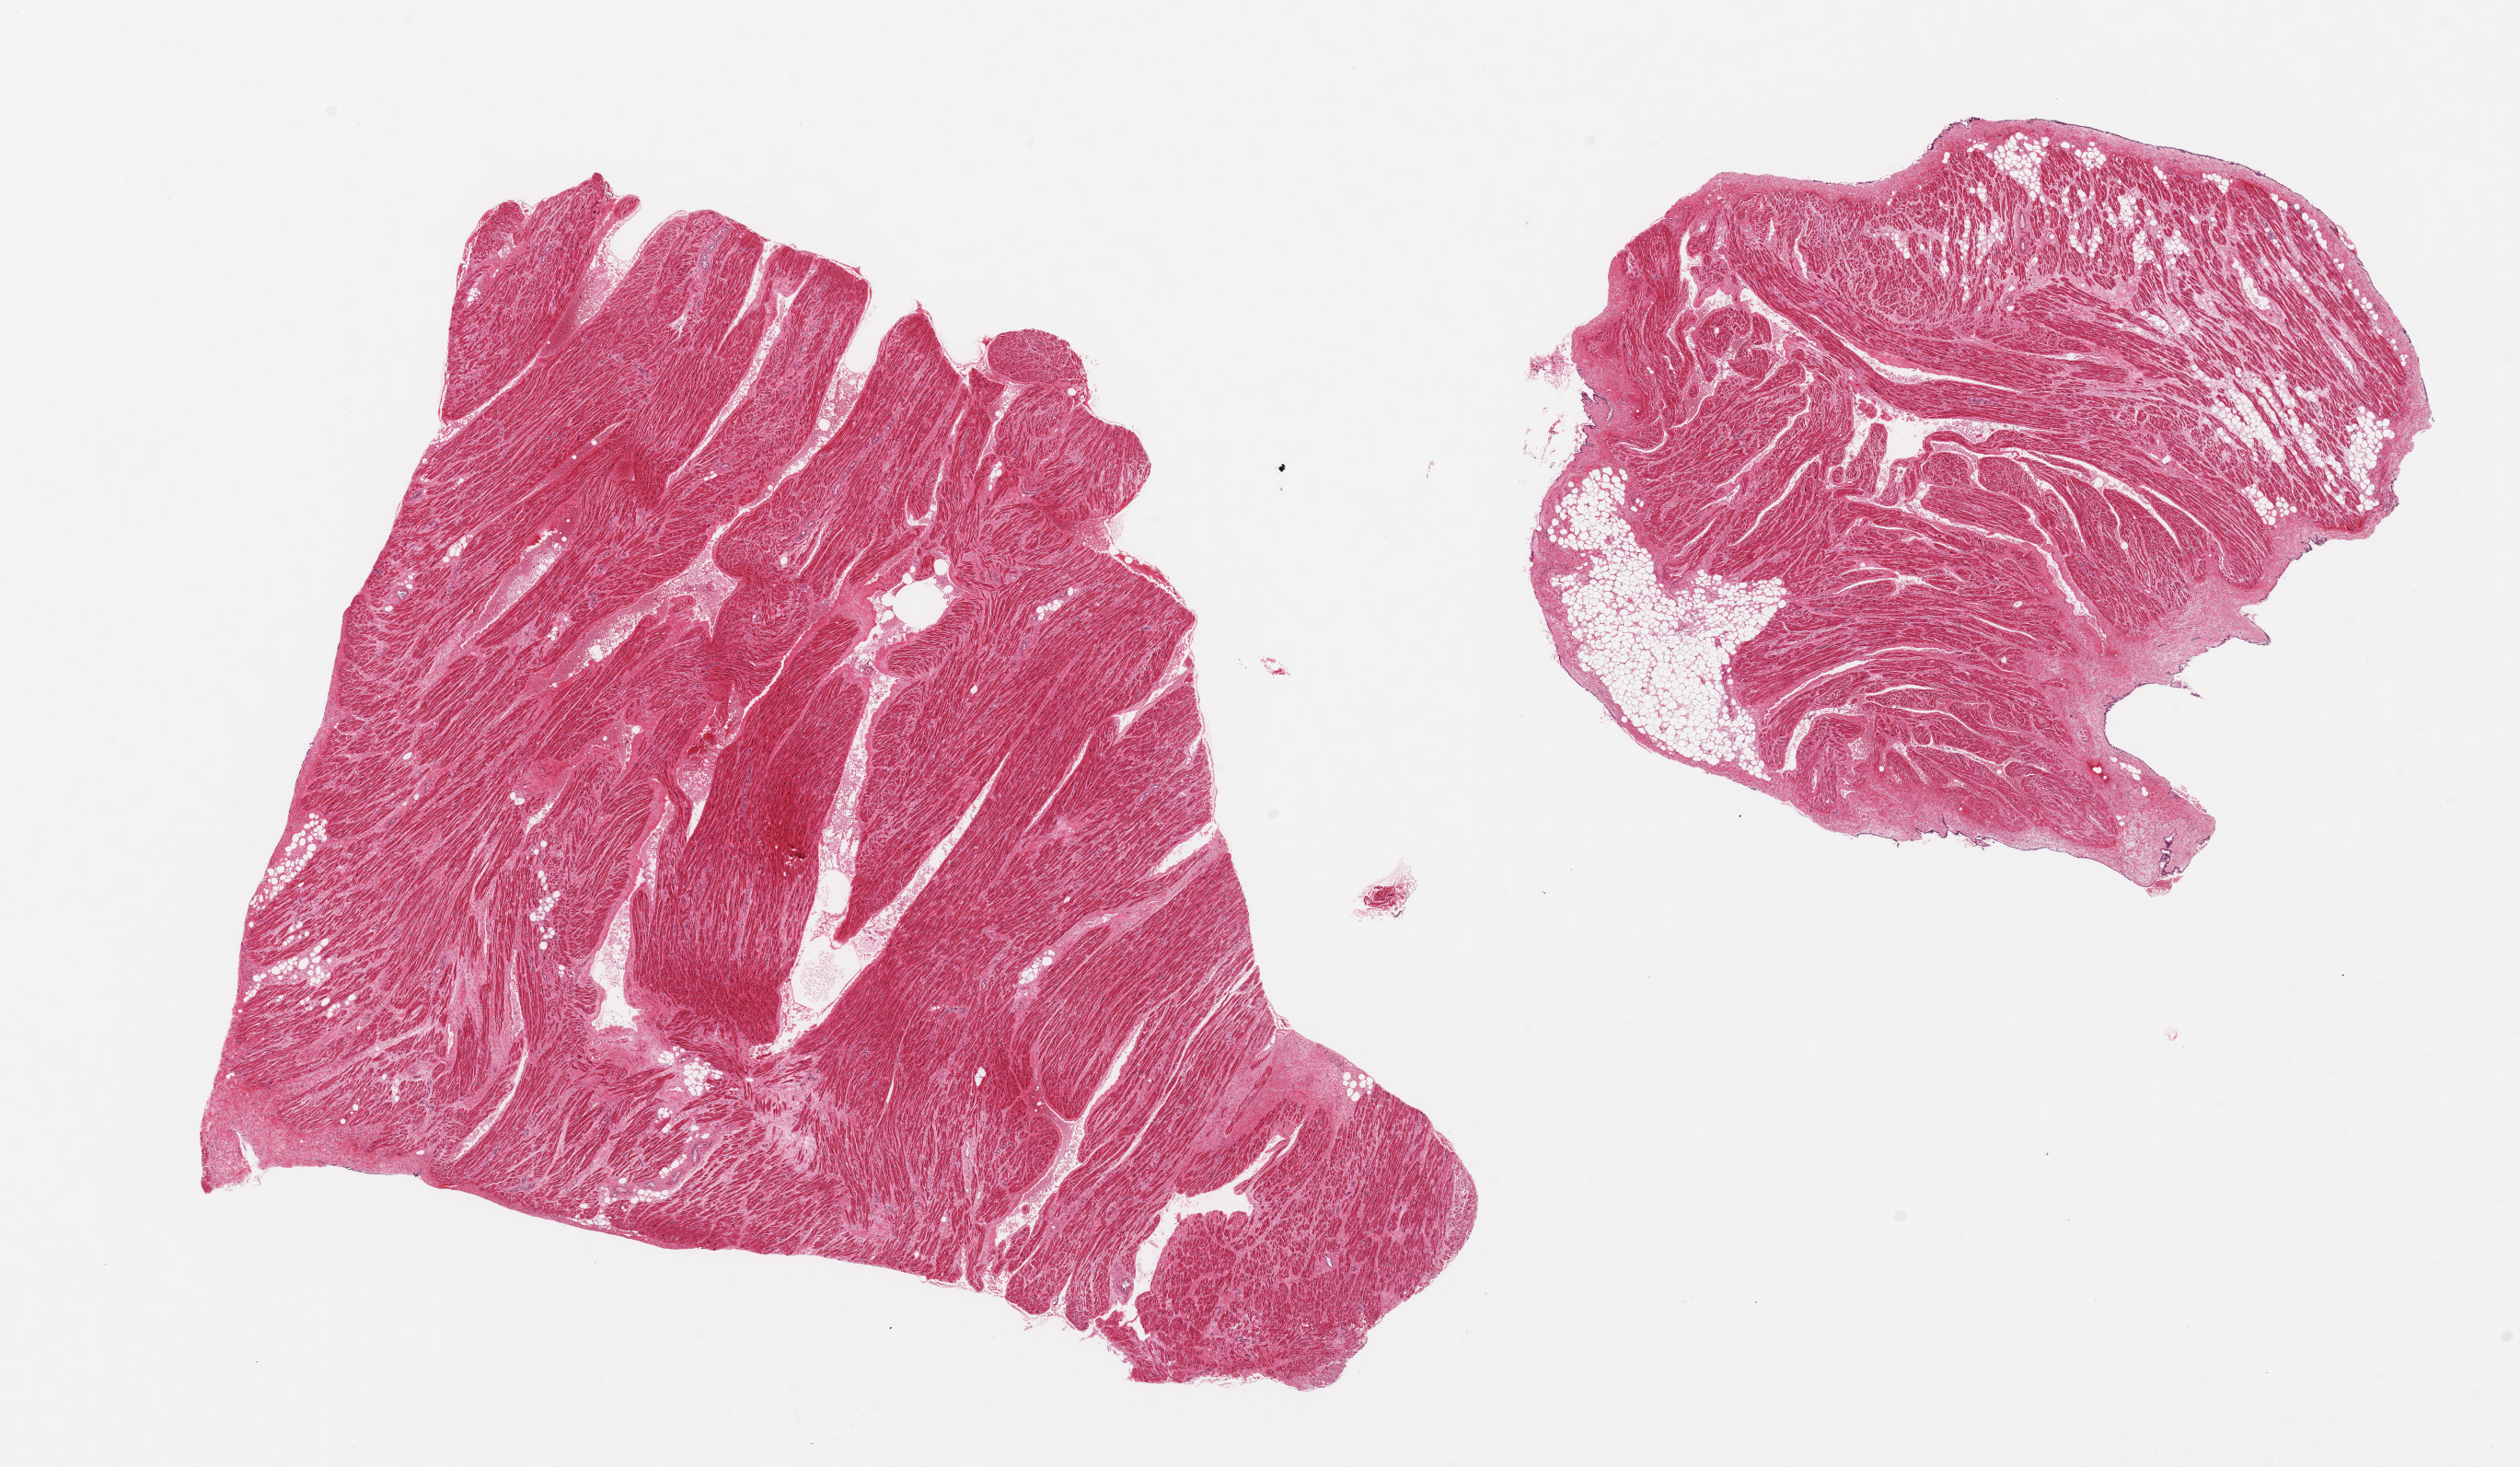
Whole-slide image, H&E stain, a low-resolution overview of the entire scanned area, about 21.7 x 12.6 mm. PAXgene-fixed, paraffin-embedded tissue. Sampled site (target tissue): auricular appendage. Donor tissue sample. Donor sex: female.
Reviewer comment on this tissue sample: 2 pieces, no abnormalities.